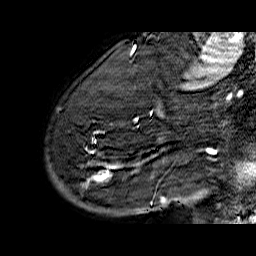
Breast MRI (dynamic contrast-enhanced), one sagittal slice. Position 48 of 60 along the scan axis. Dynamic contrast-enhanced series, time point 2 of 6 at this slice position (early post-contrast). 1.5 T. TE 6.5 ms, TR 32.9 ms. 4 mm slice thickness. 256 × 256 image matrix. Female patient. Case-level facts recorded for this patient, not image findings: setting: breast cancer imaged before/during neoadjuvant chemotherapy; receptor status: HR-positive, HER2-negative.
Outlined on this slice (semi-automatically segmented with operator editing):
- analysis volume of interest (the breast-tissue region the enhancement analysis was run in; not a lesion): bounding box (x1, y1, x2, y2) in pixels: (47, 74, 176, 210)
- tumour enhancement mask (voxels above the 100 % enhancement threshold inside the analysis volume of interest): (80, 111, 164, 202)